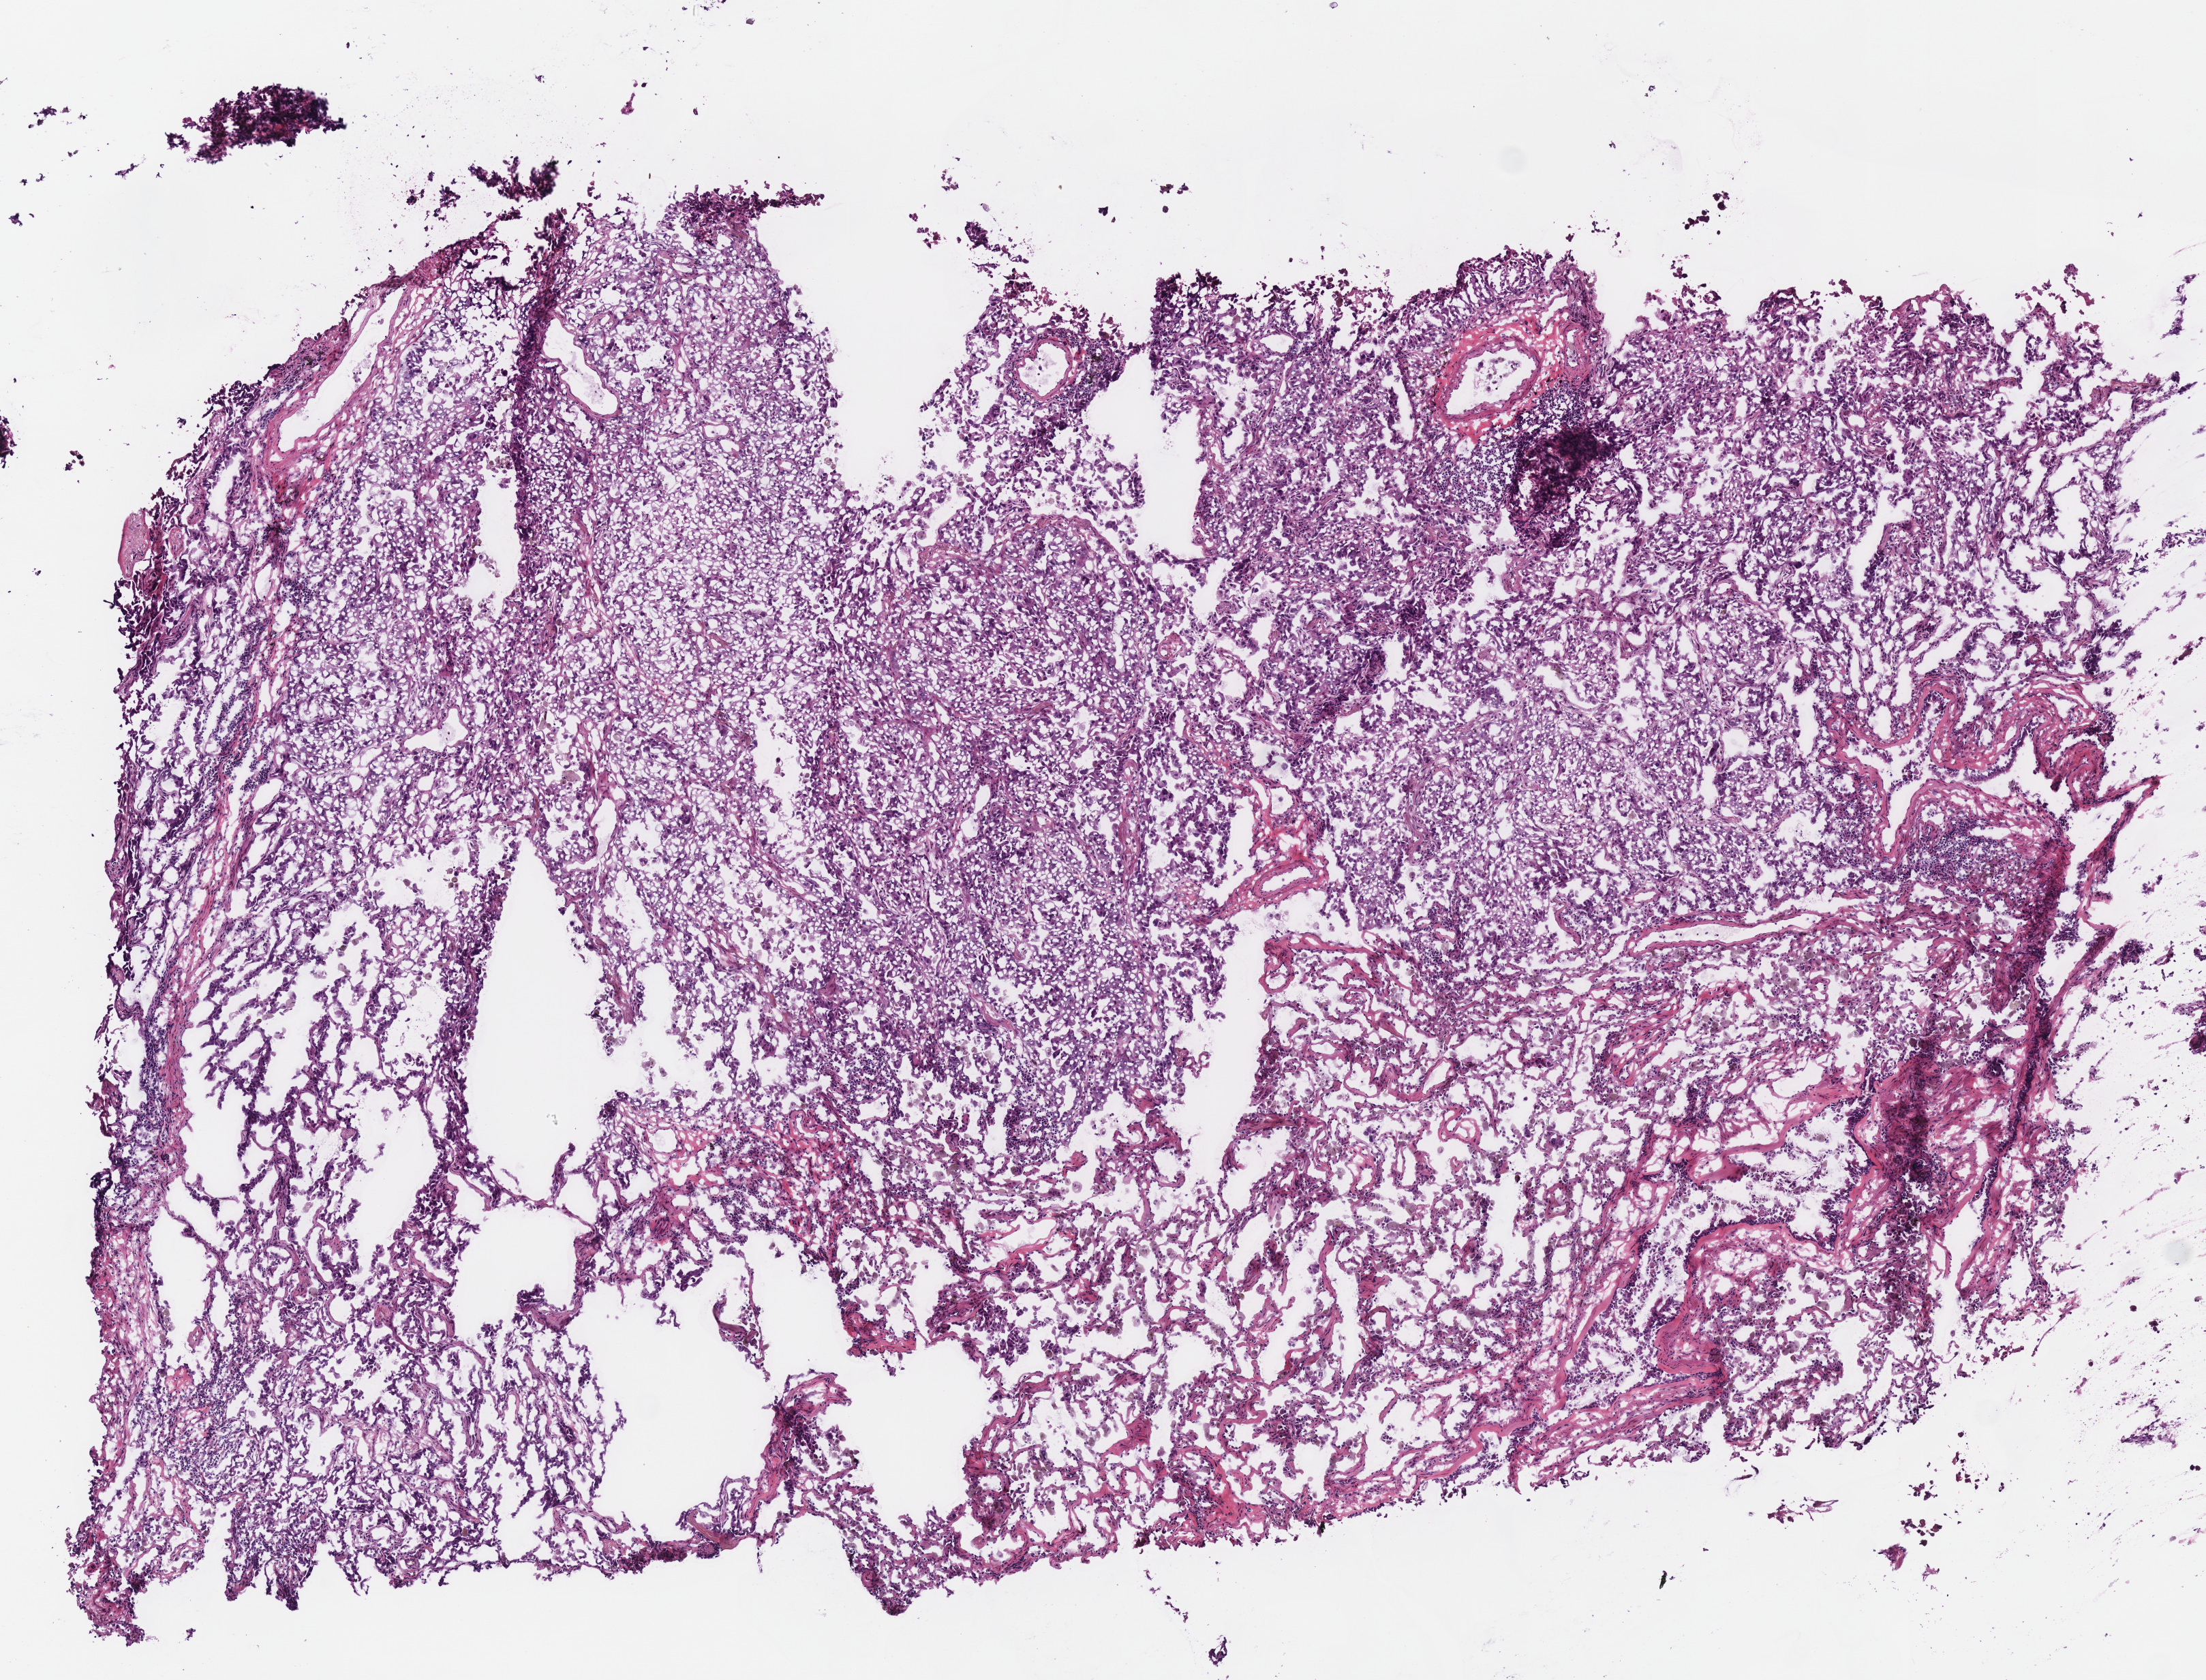
Hematoxylin and eosin (H&E) stained whole-slide image, low-resolution overview of the scanned area, about 6.4 x 4.8 mm, frozen section from the bottom of the tissue portion, primary tumour sample from the lung. Female patient; age at initial diagnosis 53 years.
Histologic diagnosis: Adenocarcinoma, NOS (upper lobe, lung).